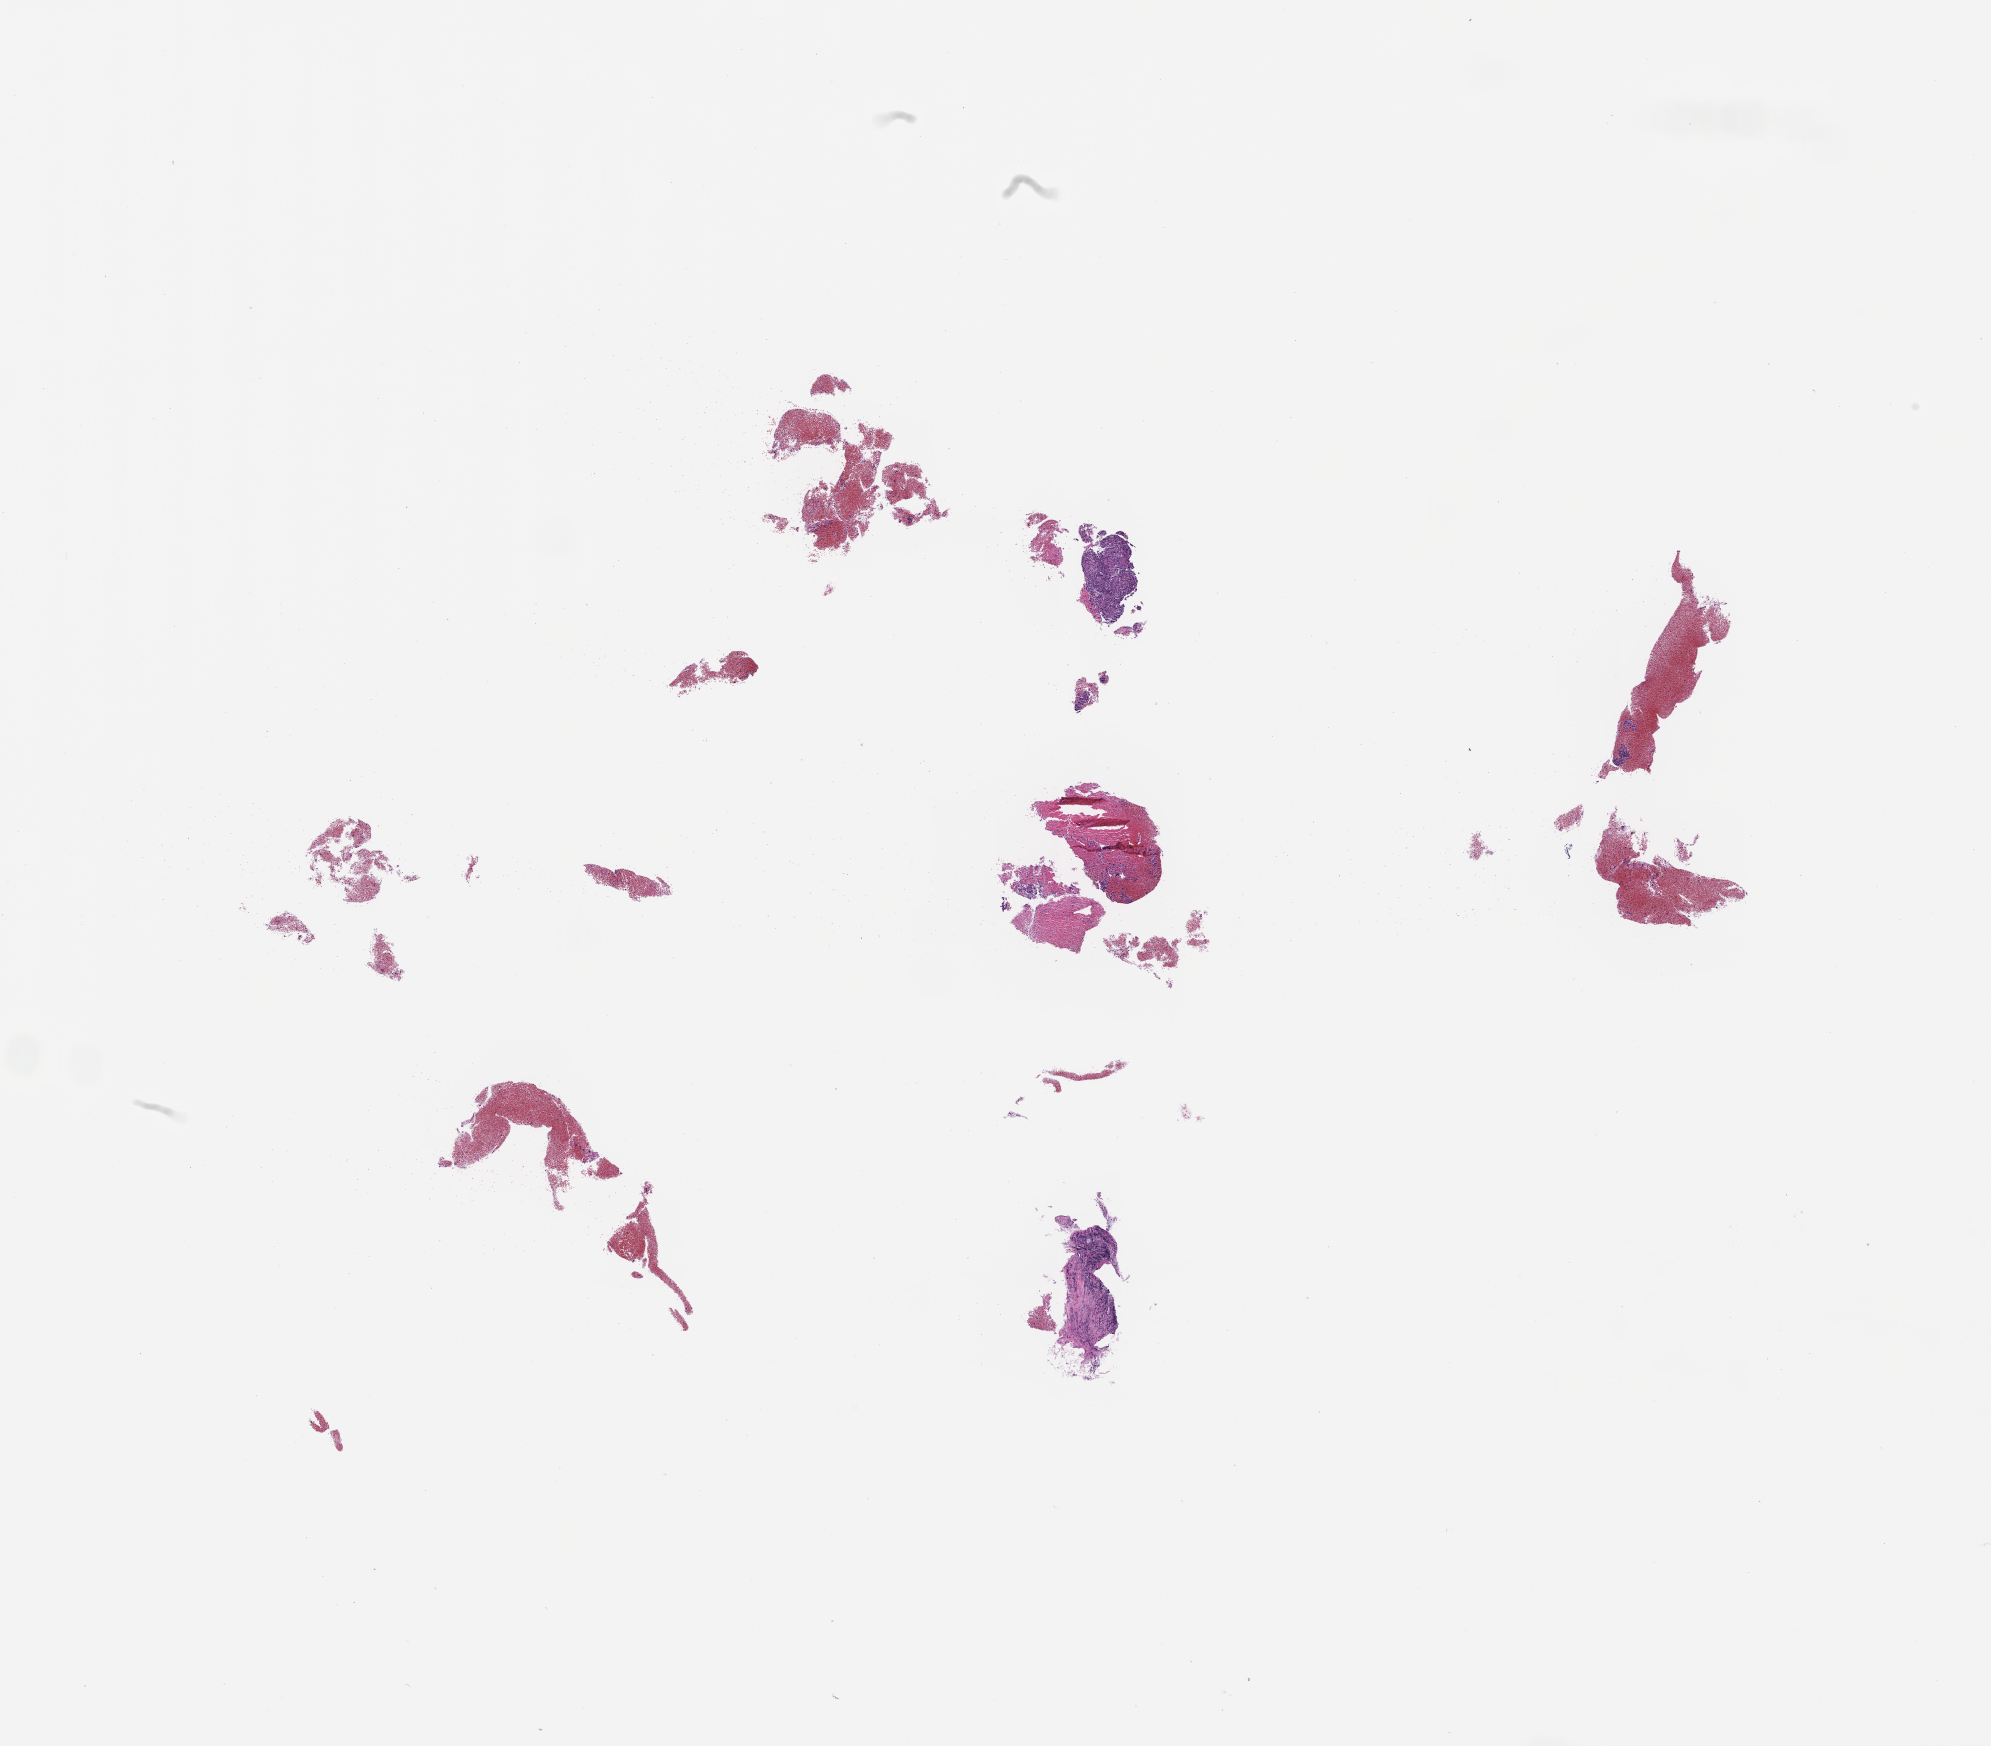
Digitized hematoxylin and eosin (H&E)-stained section — whole scanned area (about 16.1 x 14.1 mm) shown as a low-resolution overview; formalin-fixed, paraffin-embedded (FFPE) tissue; tissue site: lung. Male patient.
* this section: primary tumour tissue
* diagnosis: Non-Small Cell Lung Carcinoma